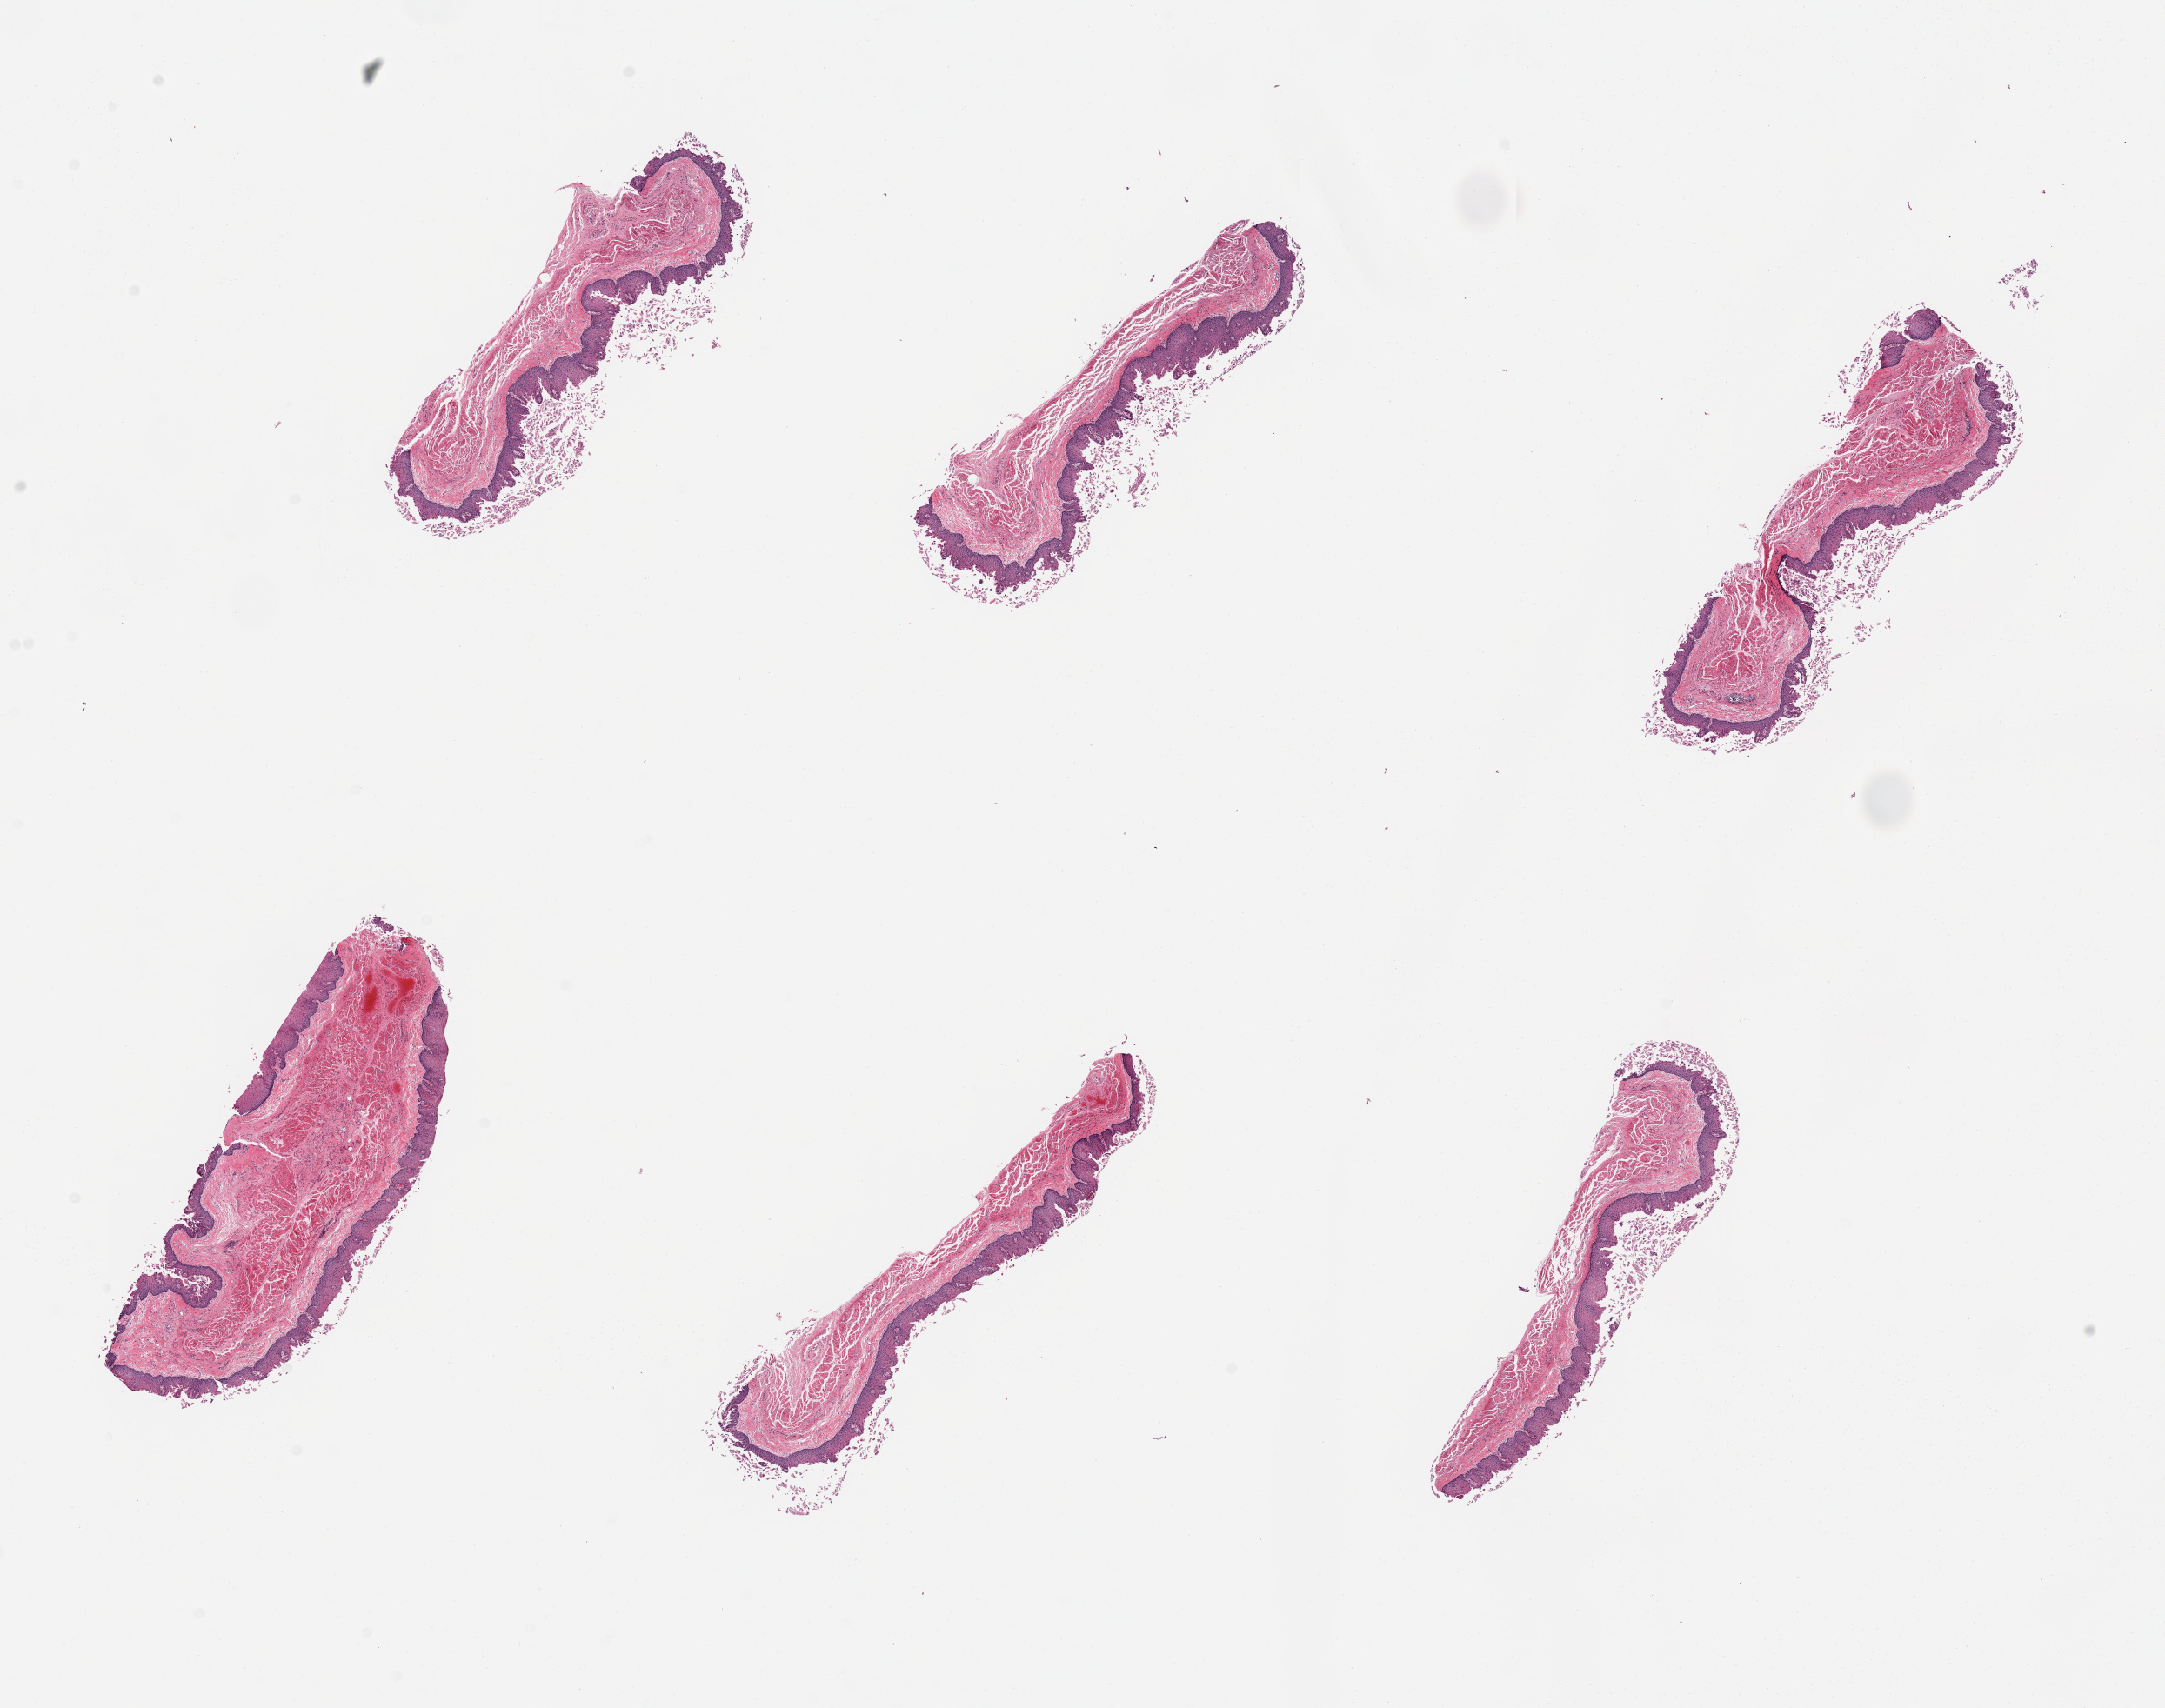
Digitized hematoxylin and eosin (H&E)-stained section, brightfield, a low-resolution overview of the entire scanned area, about 19.7 x 15.5 mm (slide scanned at 20x). PAXgene-fixed paraffin-embedded (PFPE) section. Target tissue: esophageal mucous membrane. Tissue donor sample. Donor: male.
- reviewer comment on this tissue sample: 6 pieces, squamous mucosa is ~20-30% thickness